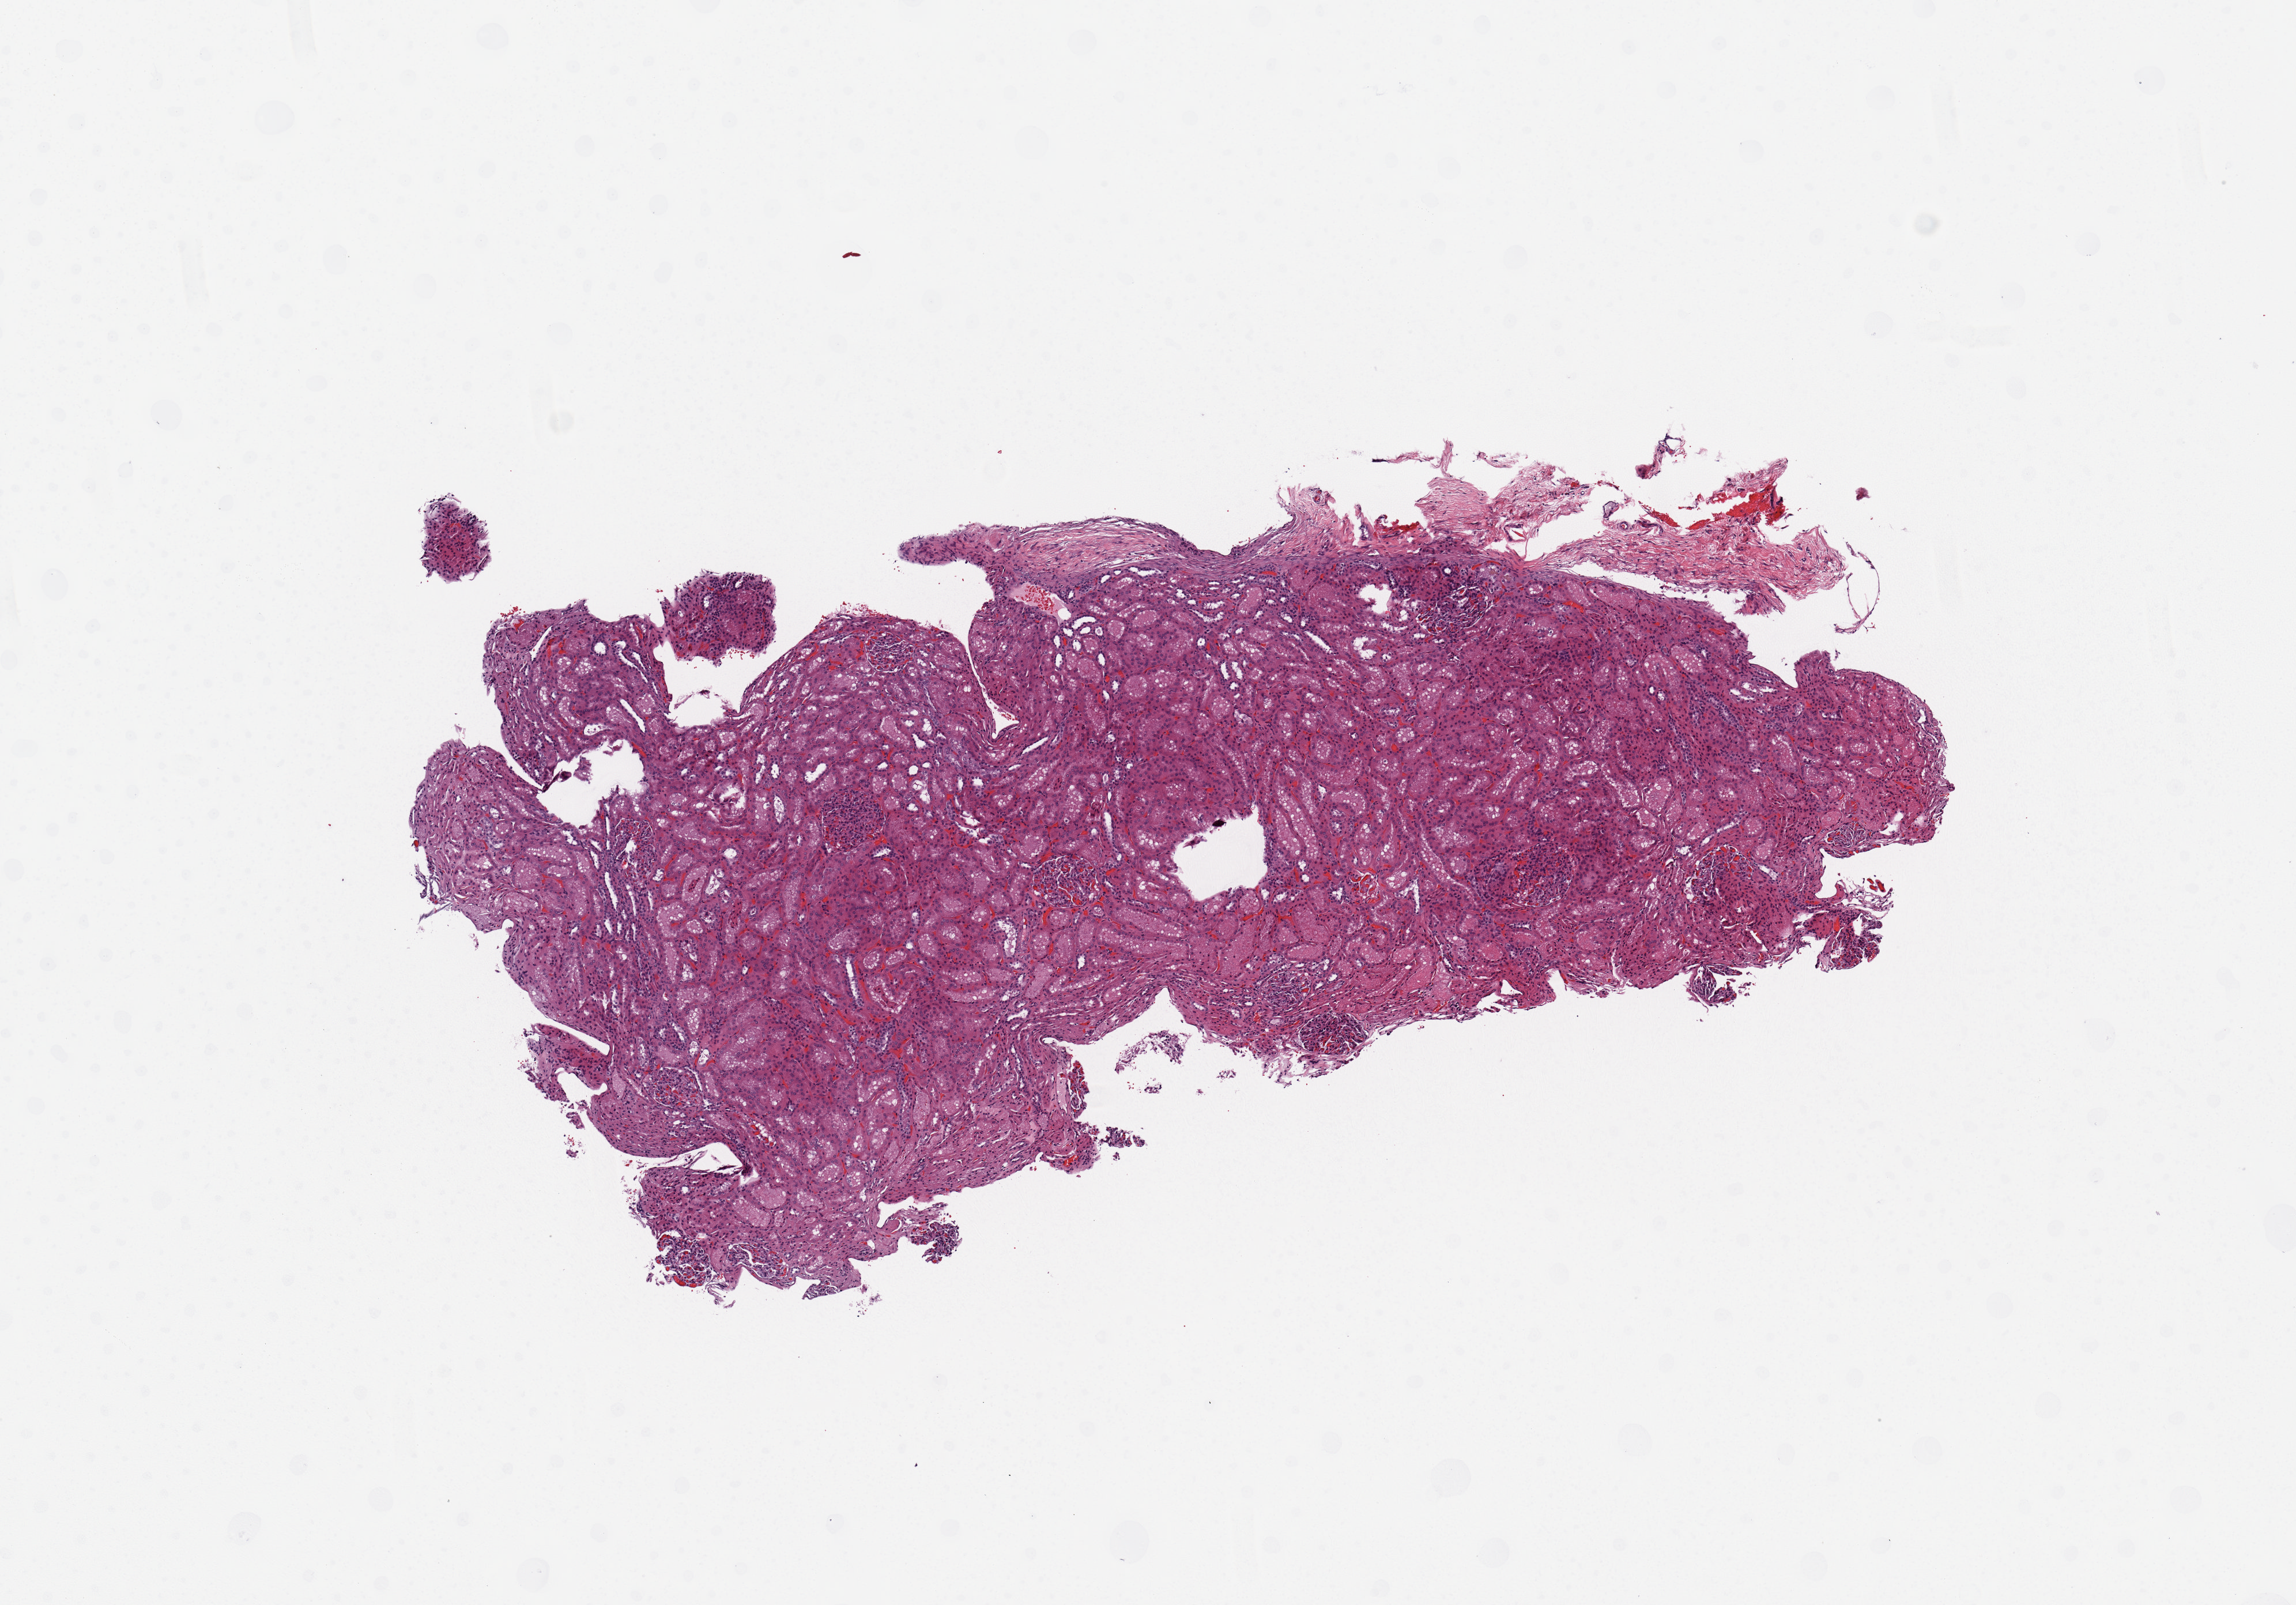
Digitized H&E tissue section (whole slide) — shown as a low-resolution overview of the whole scanned area (about 7.9 x 5.5 mm, acquisition: 20x scan). Normal (non-tumour) tissue sample, kidney. 33-year-old female patient.
- this section: normal (non-tumour) tissue from the same patient
- patient diagnosis: Renal cell carcinoma, NOS